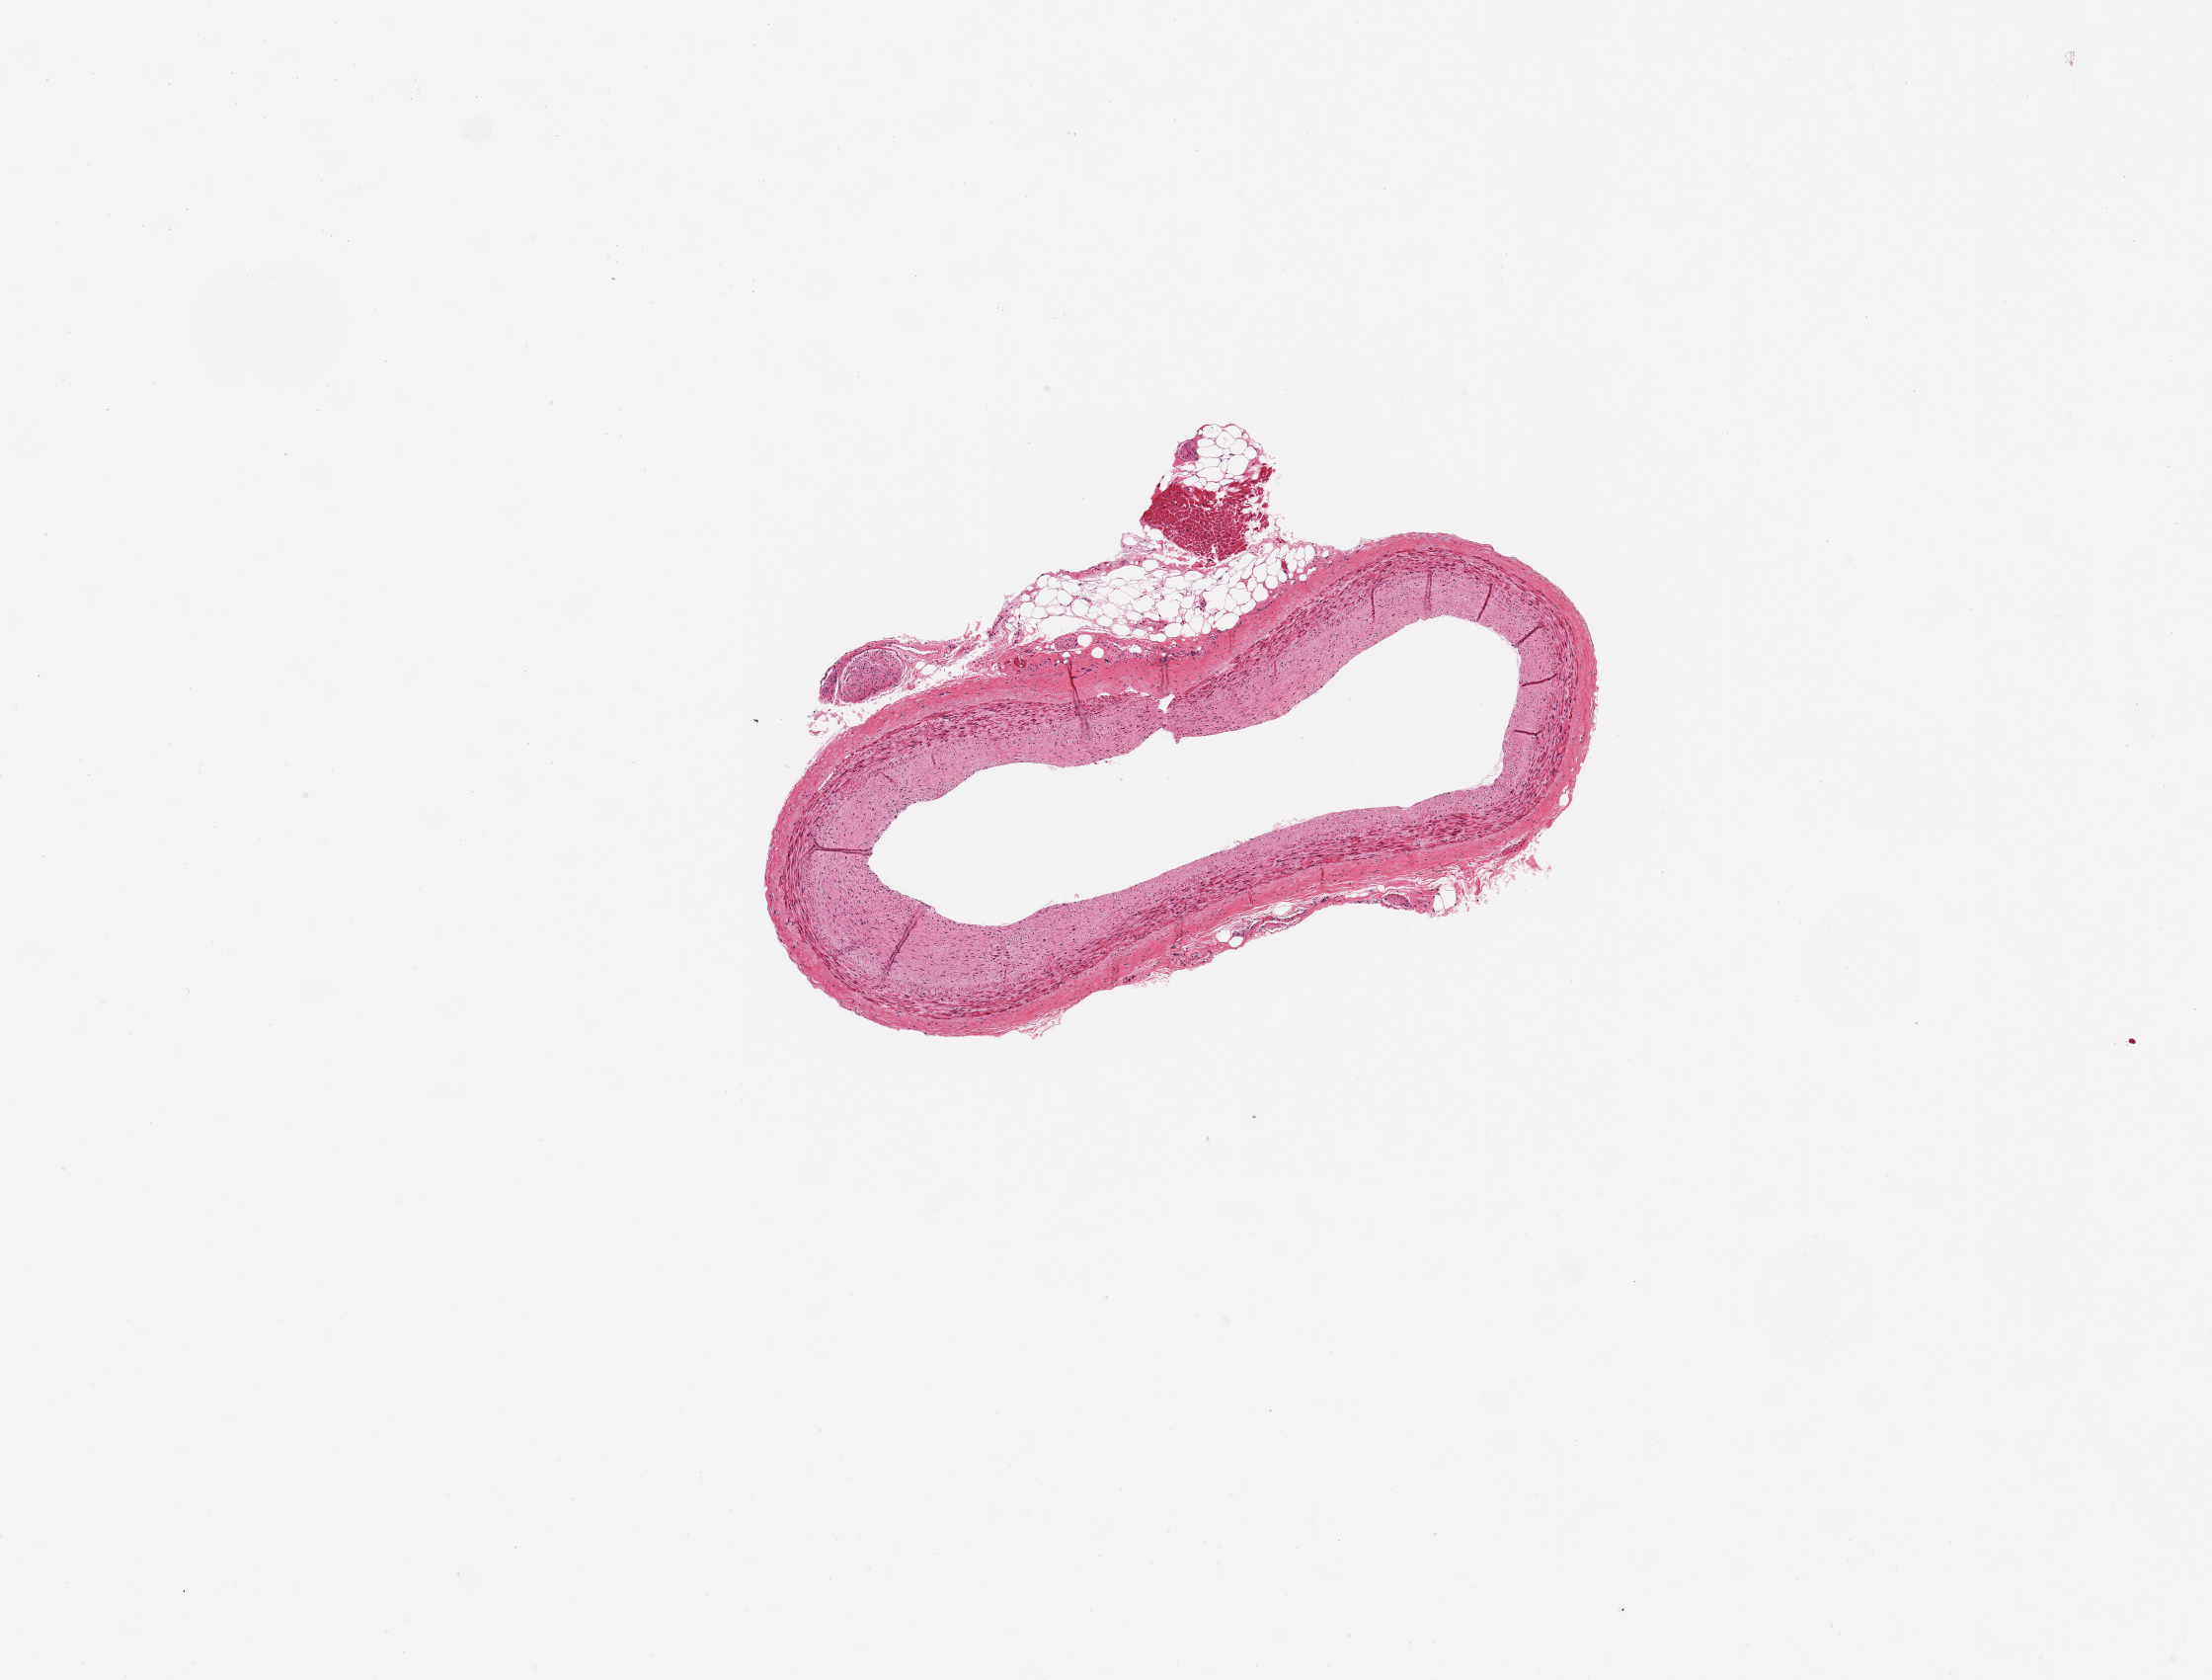
Digitized hematoxylin and eosin (H&E)-stained section — shown as a low-resolution overview of the whole scanned area (about 8.9 x 6.7 mm). PAXgene-fixed, paraffin-embedded tissue. Sampled site (target tissue): coronary artery. Tissue donor sample.
Reviewer comment on this tissue sample: 1 piece, 3x2mm; mild fibroatheromatous thickening.